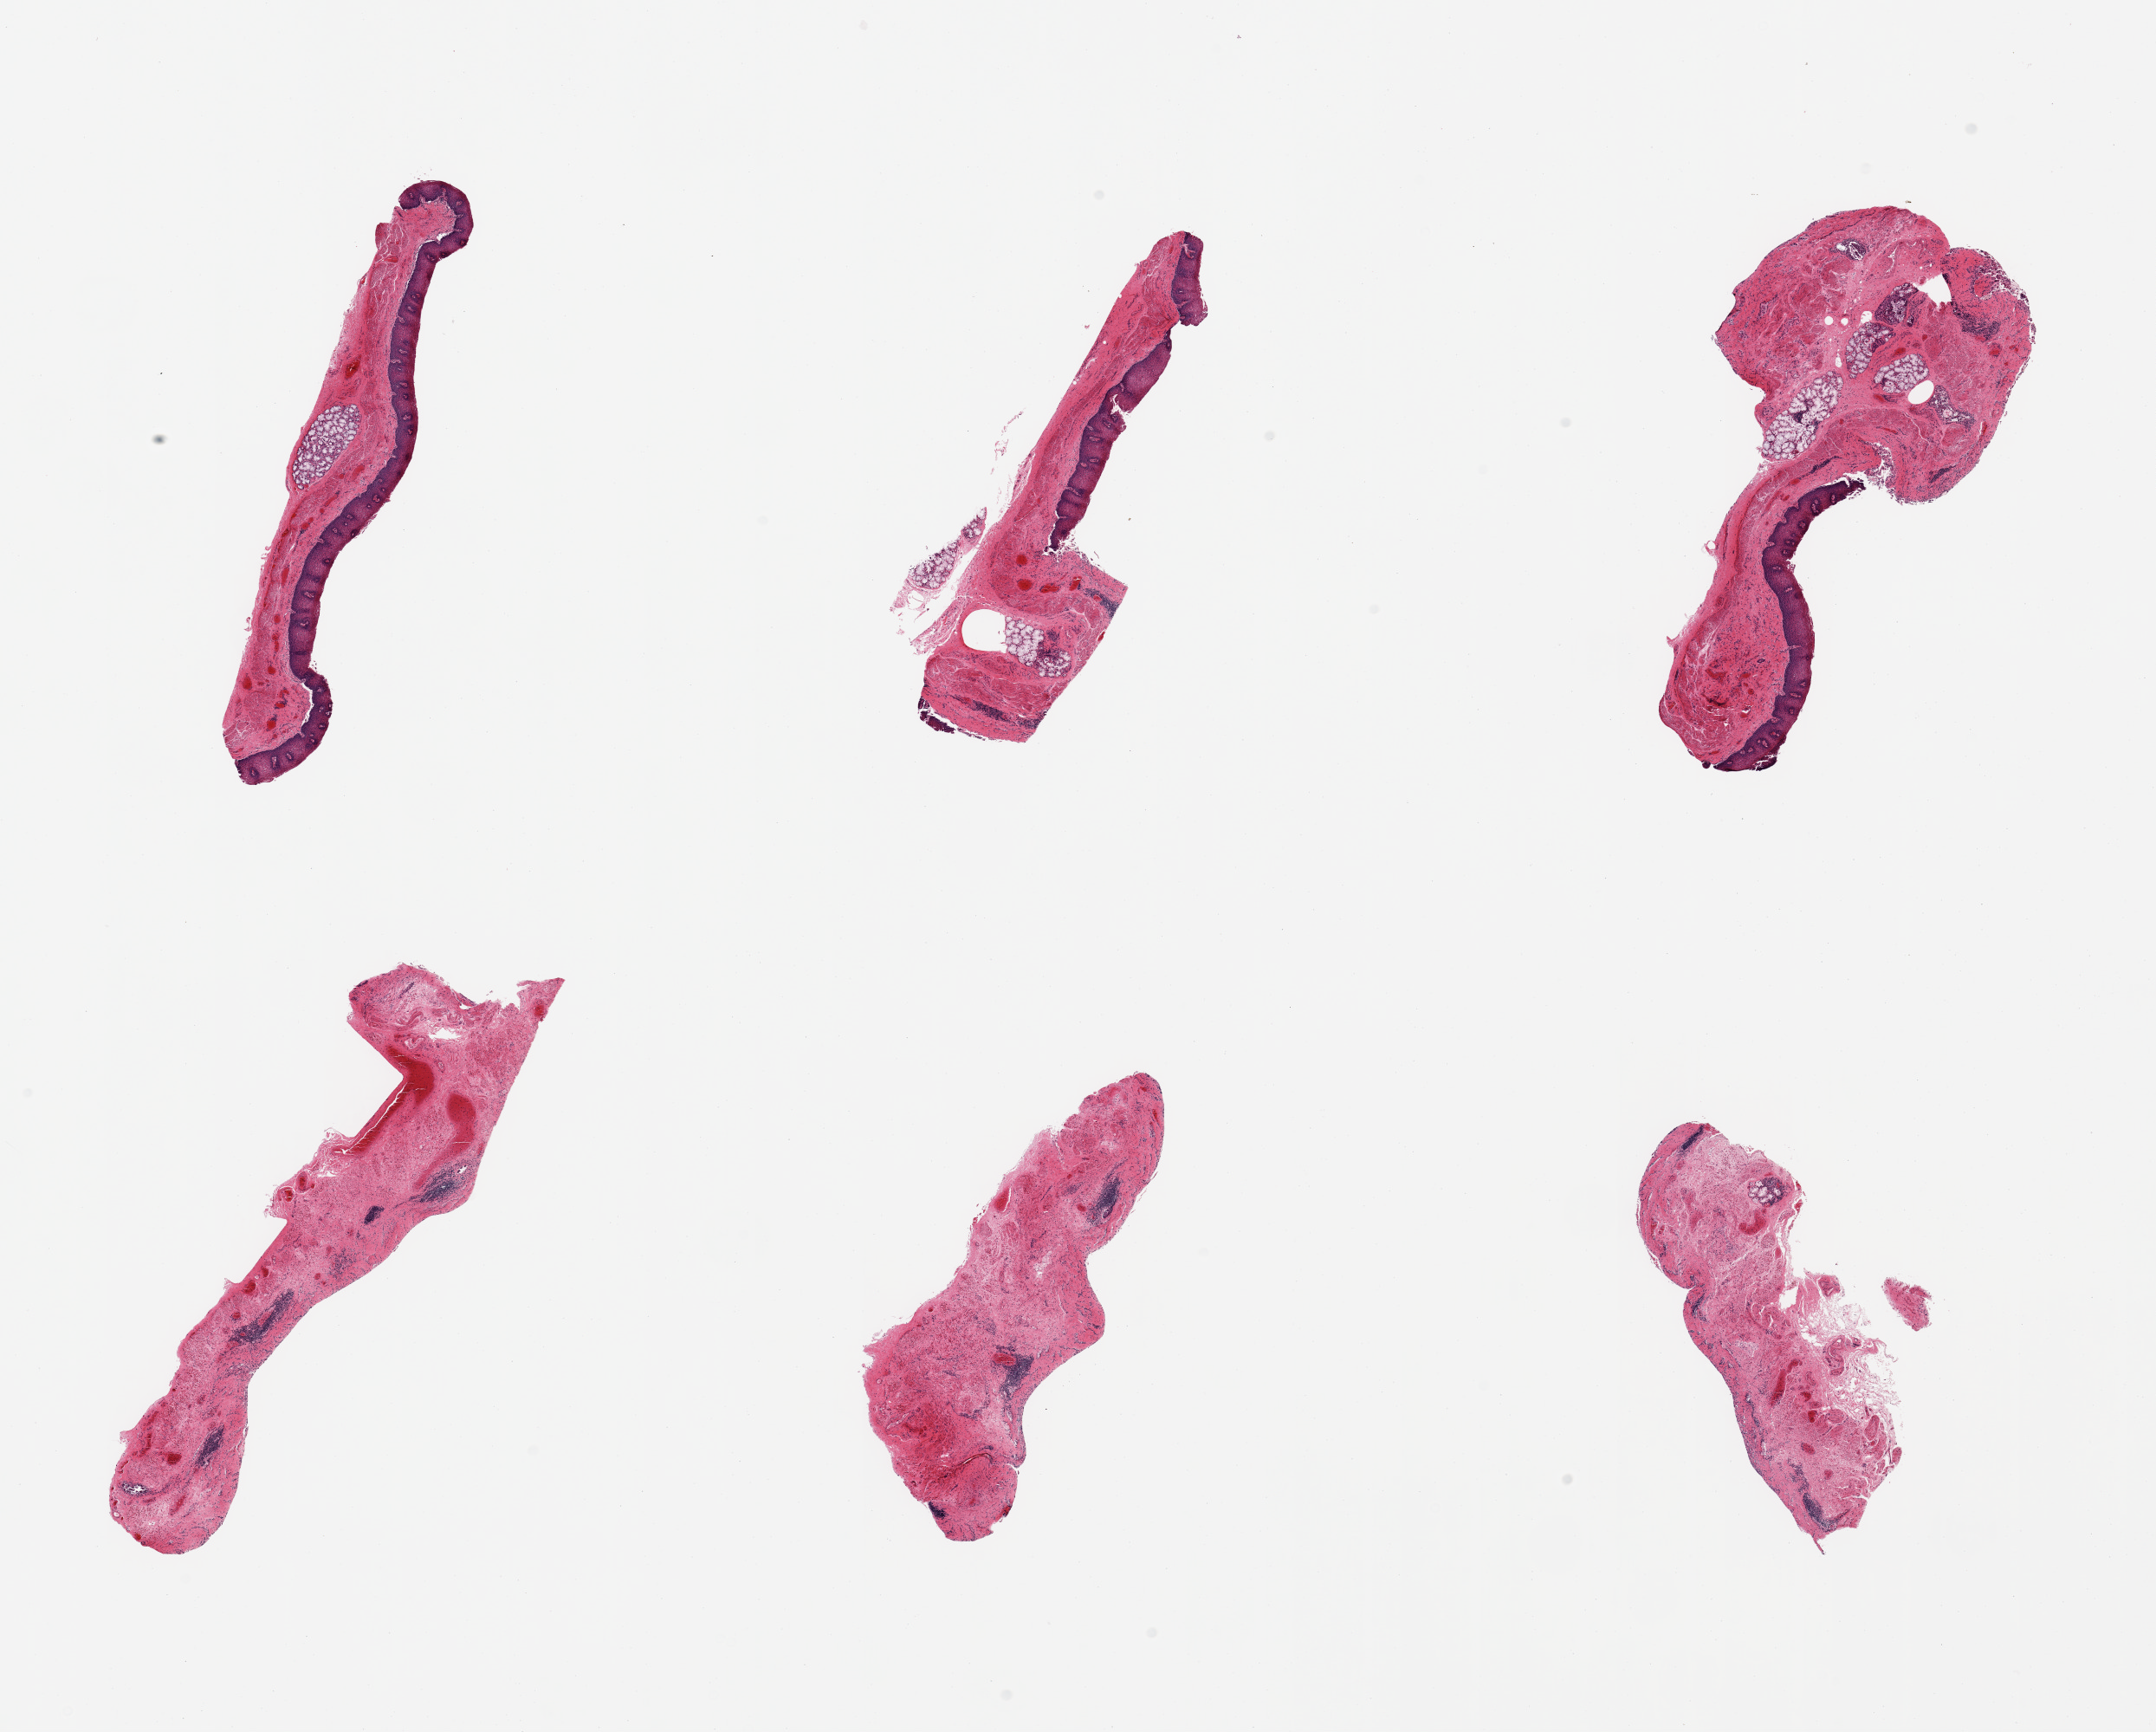
Haematoxylin and eosin whole-slide image — whole scanned area (about 19.7 x 15.8 mm, from a 20x scan) shown as a low-resolution overview. PAXgene-fixed, paraffin-embedded tissue. Section of esophageal mucous membrane (target tissue). Donor tissue sample.
Reviewer comment on this tissue sample: 6 pieces; 3 with and 3 without epithelium; several foci of chronic inflammation.